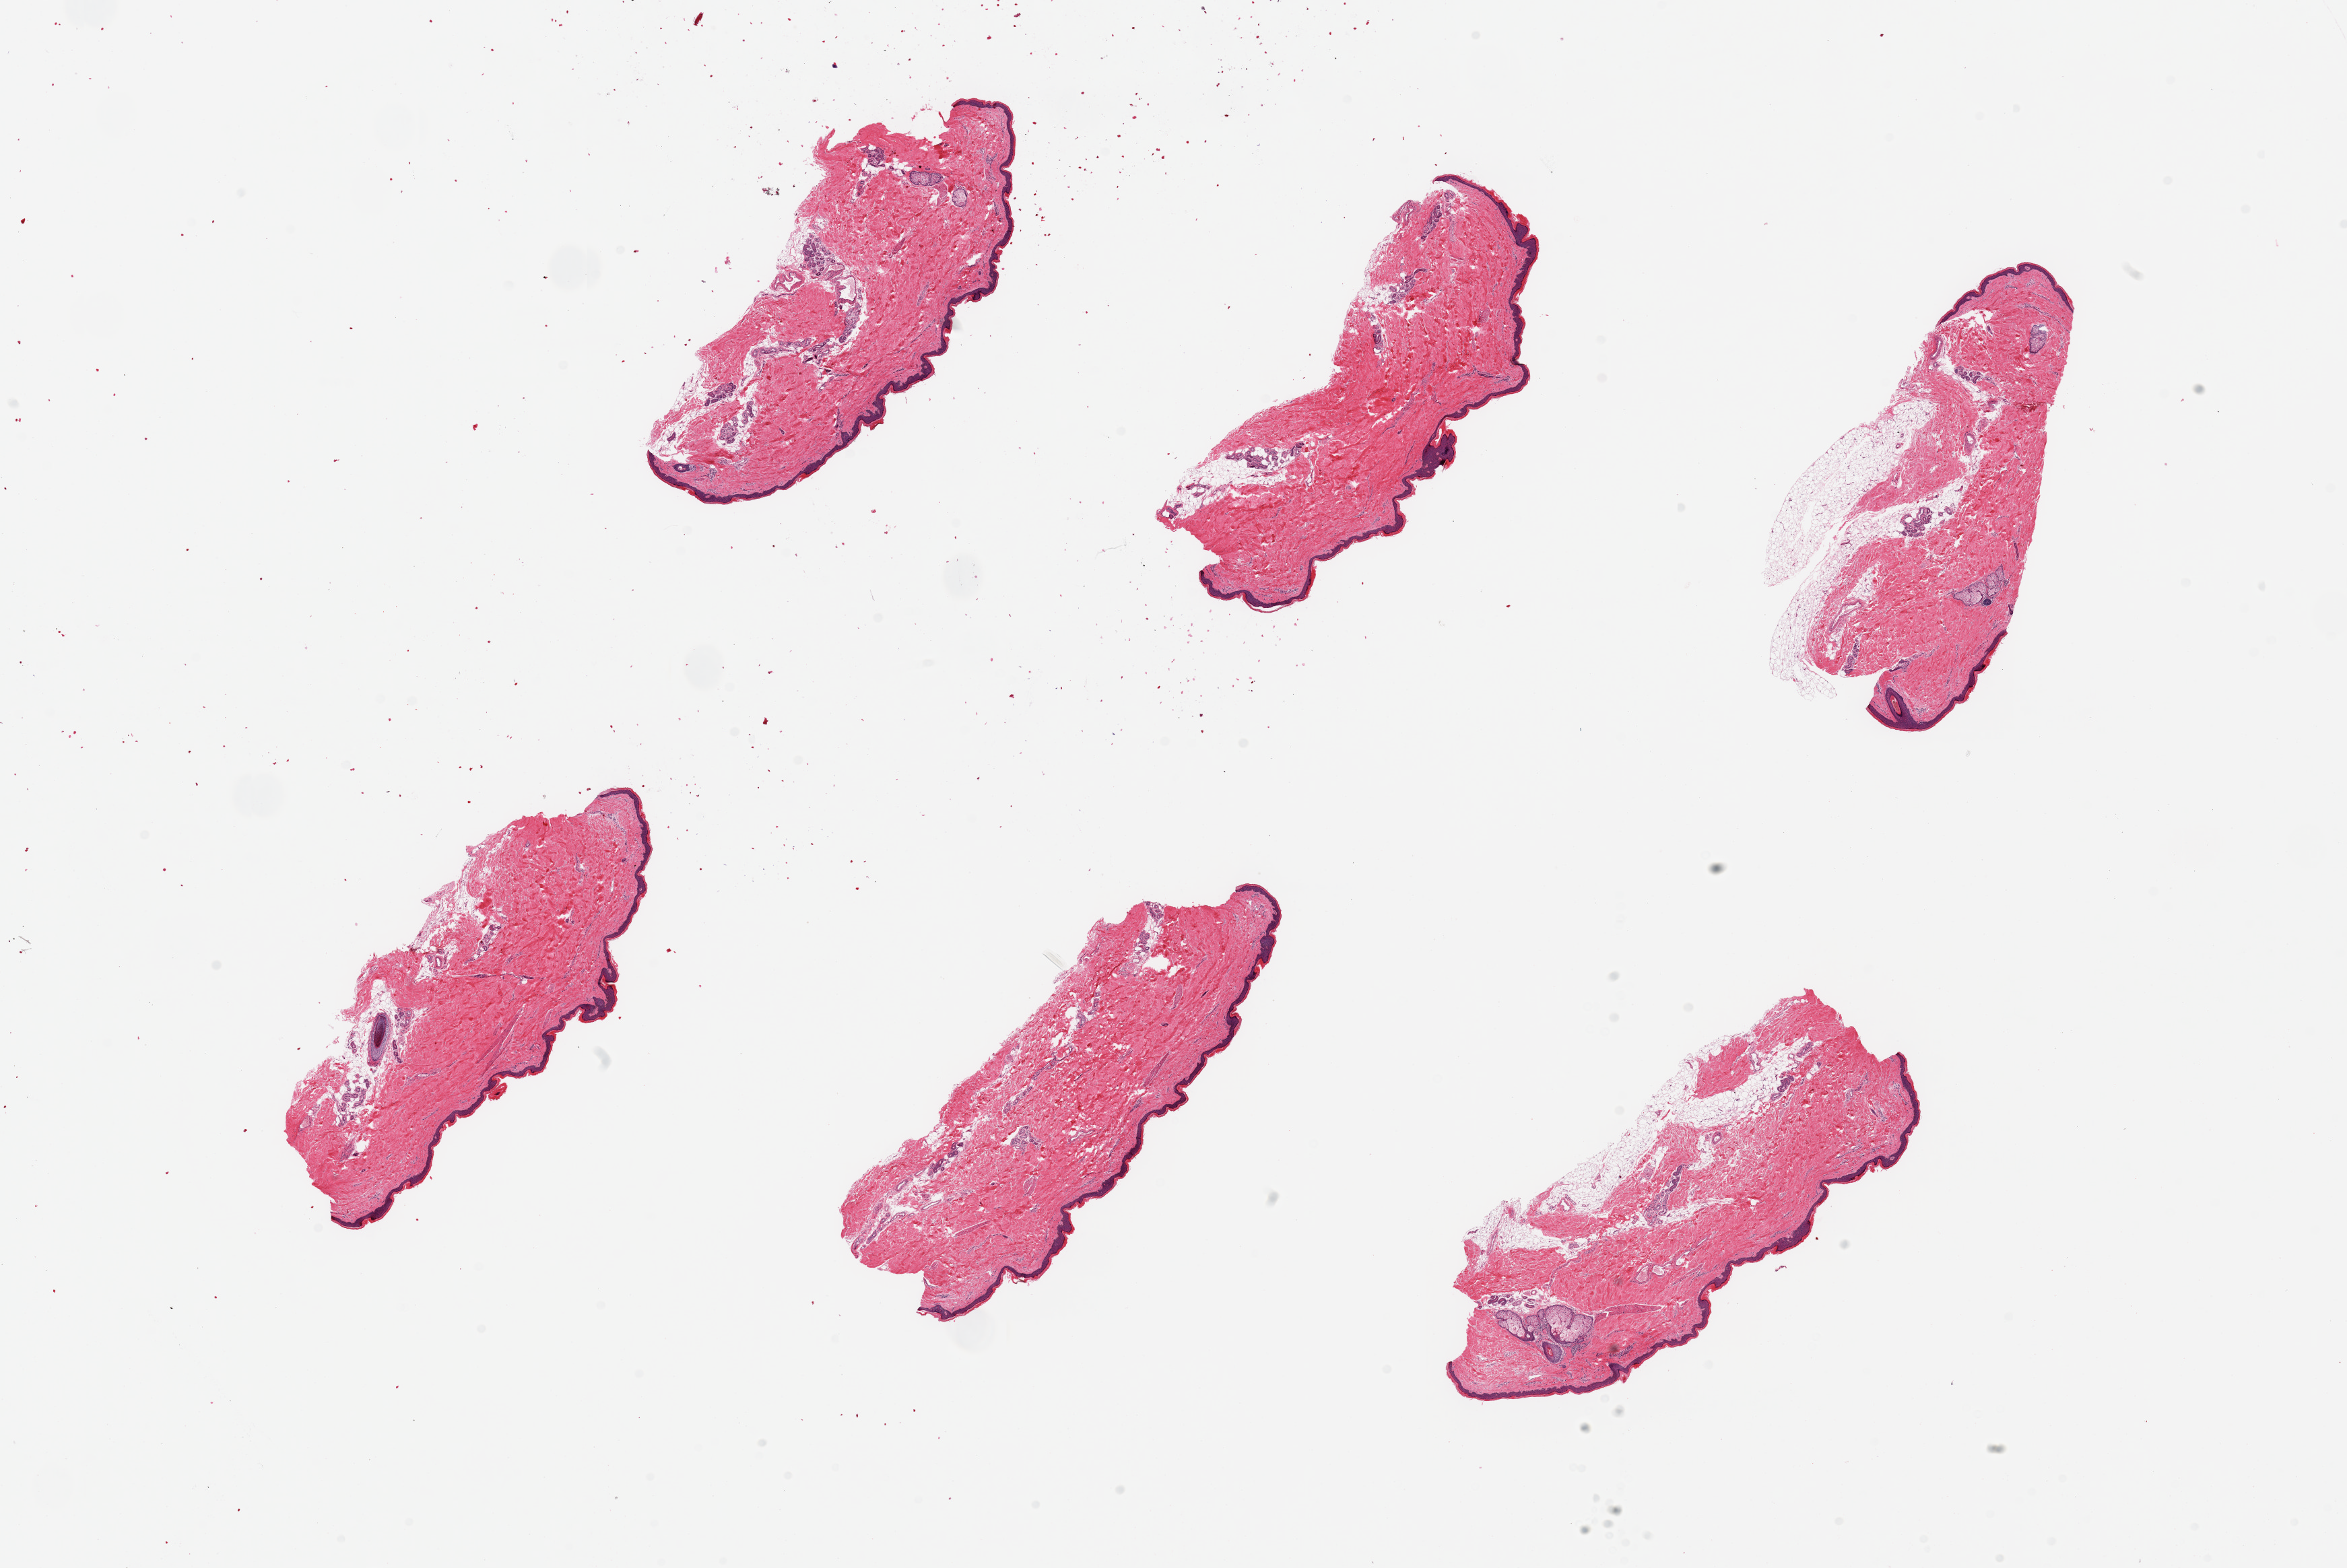
Digitized haematoxylin and eosin-stained section, brightfield, a low-resolution overview of the entire scanned area, about 27.6 x 18.4 mm. PAXgene-fixed, paraffin-embedded tissue. Target tissue: skin of lower leg. Donor tissue sample. Donor sex: male.
Pathologist's review note for this sample: 6 pieces, up to 6.5x3mm; squamous epithelium is ~2-3% thickness.